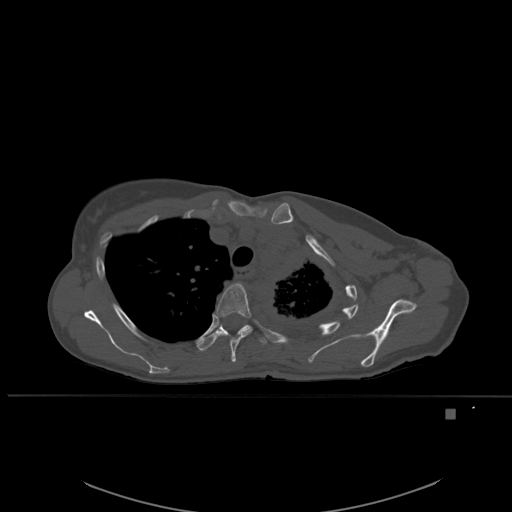
CT including the spine, one axial slice. Position 408 of 537 along the scan axis. Bone window (W 1800 / L 400 HU). 1.5 mm slice thickness. 512 × 512 image matrix, field of view 440 × 440 mm. Patient: female, 45 years. Case-level facts recorded for this patient, not image findings: primary cancer: lung.
Annotated regions visible in this slice (semi-automatic segmentation, software-assisted and operator-edited):
- T4 vertebra: bounding box <216,282,252,363> (left, top, right, bottom; pixels)
- T5 vertebra: <196,318,268,352>